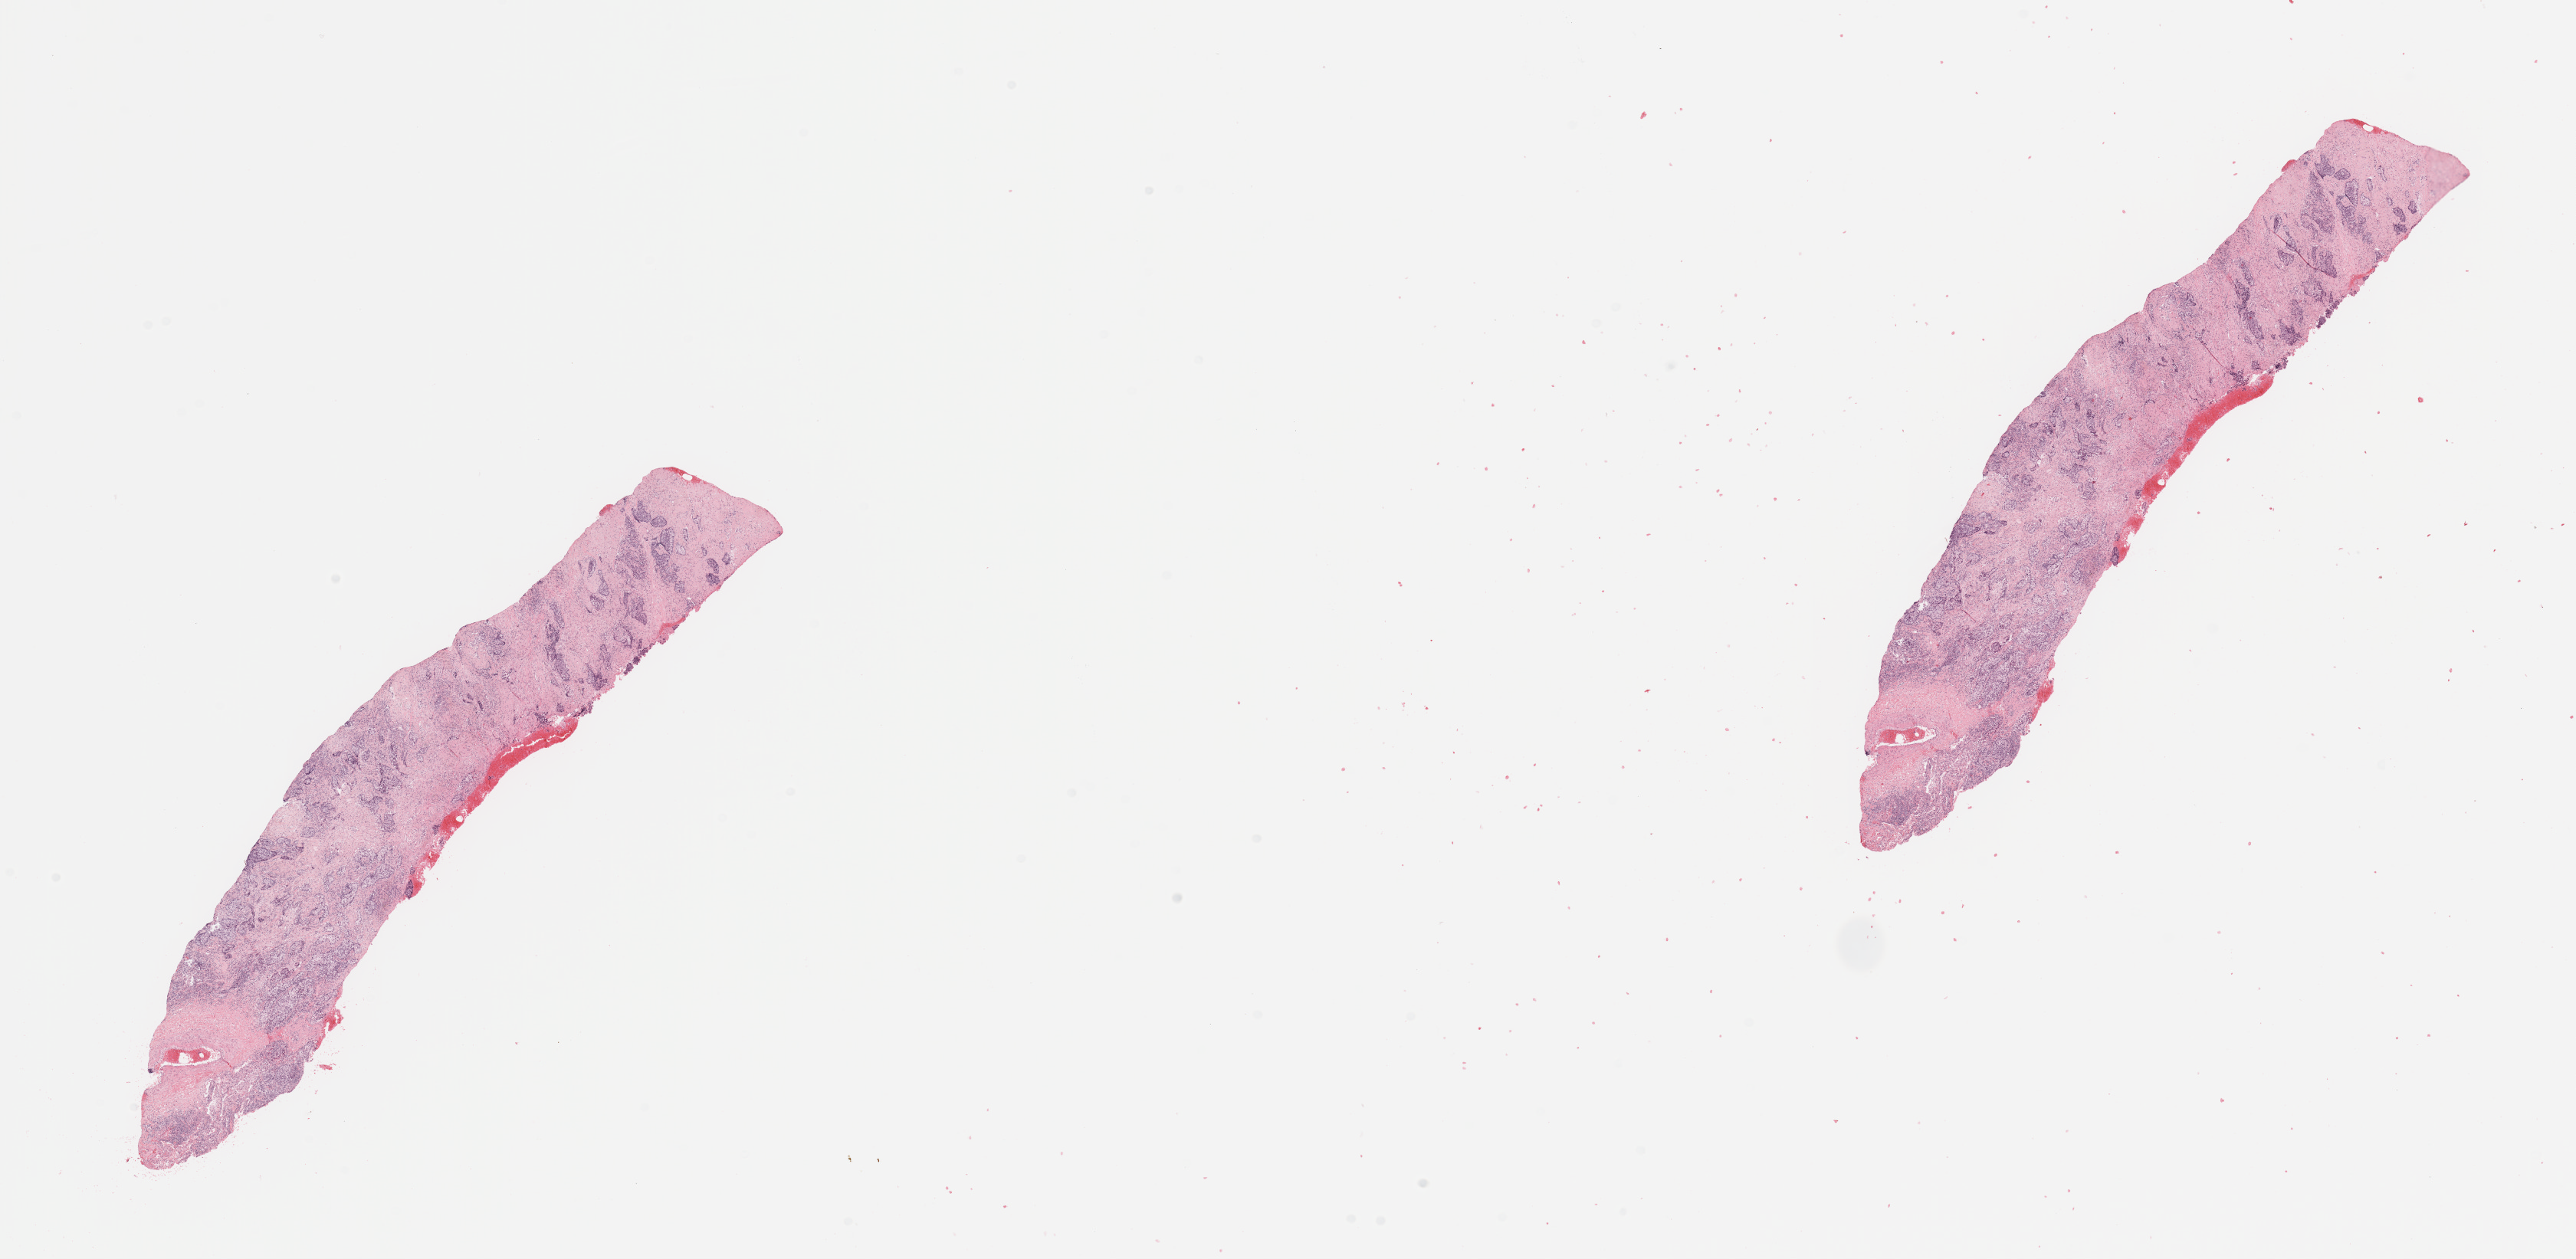
Whole-slide histology image, H&E — shown as a low-resolution overview of the whole scanned area (about 26.6 x 13.0 mm, slide scanned at 20x), lung, tumour tissue. Patient: male, age 71 years. Histologic grade: G2 (moderately differentiated).
* primary tumour site (as recorded): left upper lobe
* AJCC pathologic stage: IA
* diagnosis: Adenocarcinoma, NOS